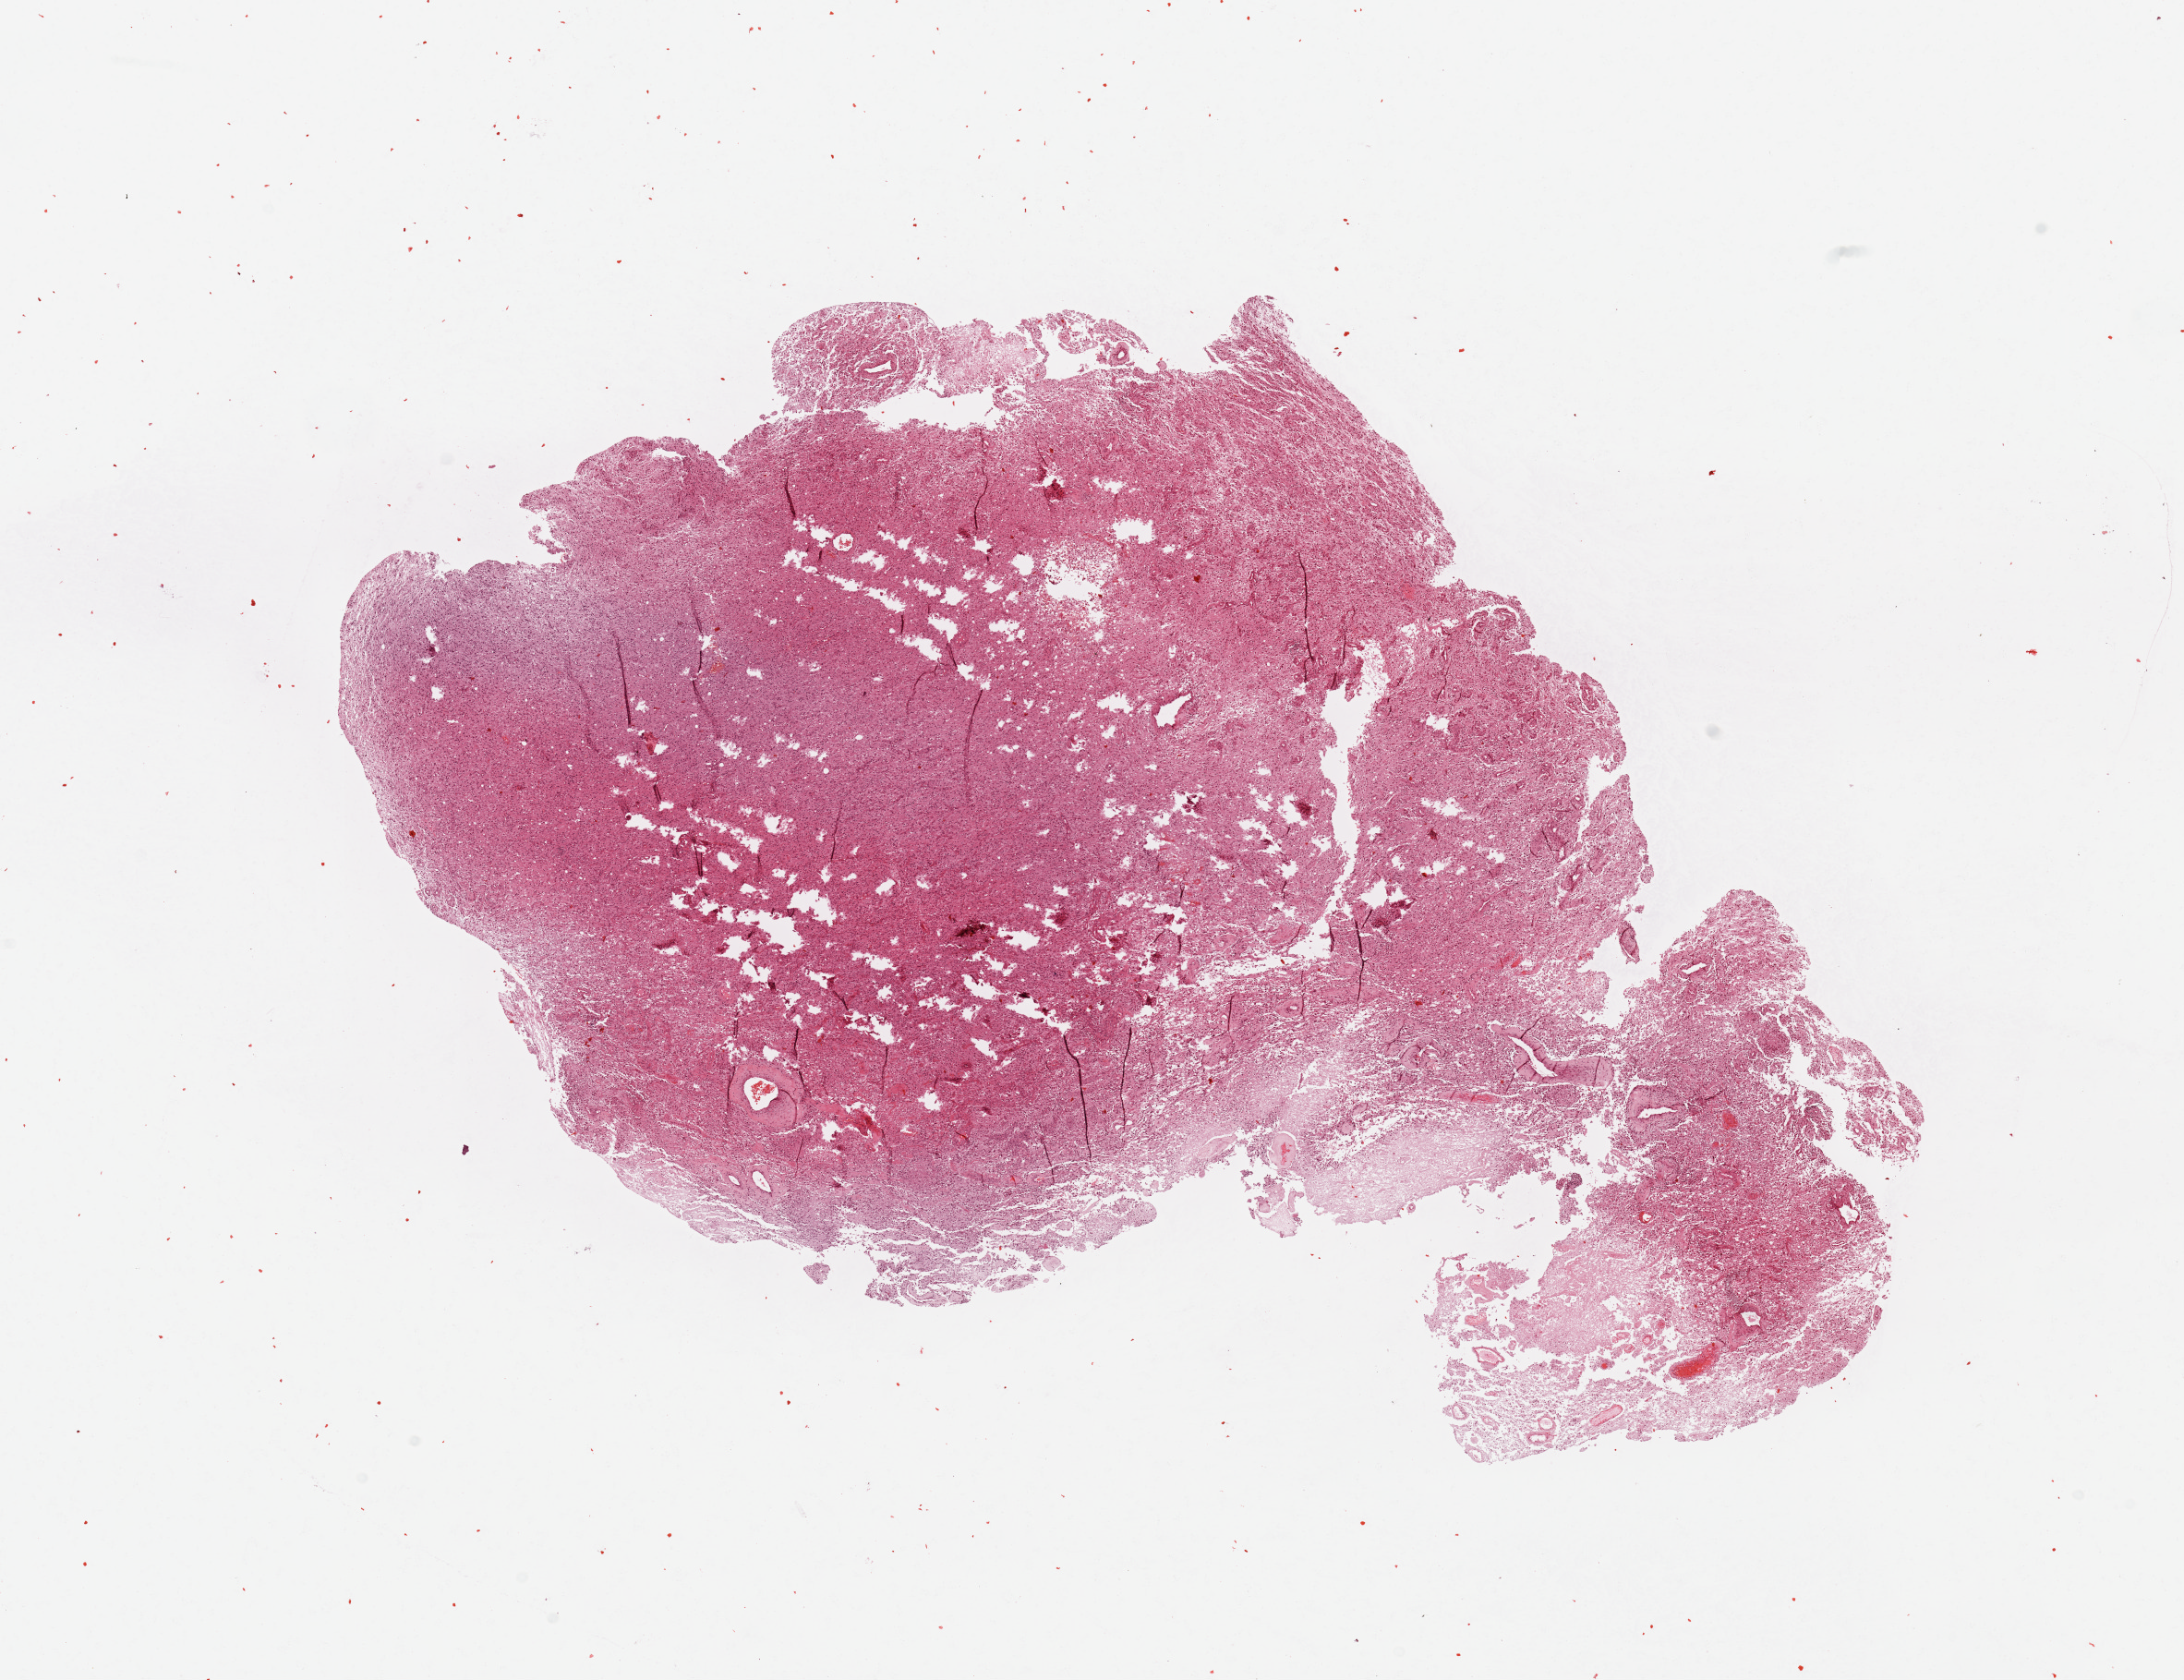
Digitized Hematoxylin and eosin (H&E) stained tissue section (whole slide), low-resolution overview of the scanned area, about 18.7 x 14.4 mm (slide scanned at 20x). Tumour tissue sample, sampled site: brain. 71-year-old female patient. Pathologist review of this section (percent, as recorded): tumour nuclei 75%, necrosis 15%.
Histologic diagnosis: Glioblastoma.